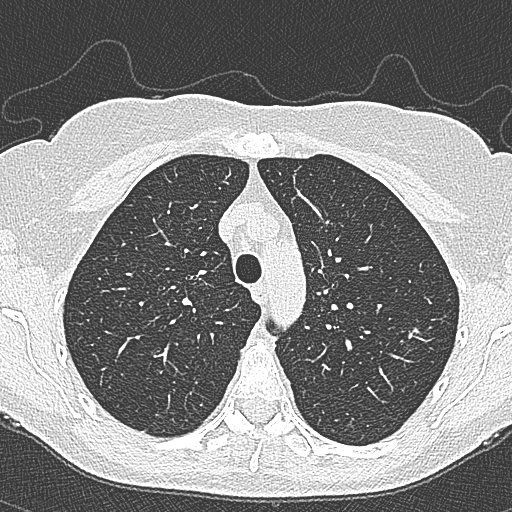
Chest CT (low-dose screening protocol), one axial image. Second annual screen. Lung window (W 1500 / L -600 HU). 1 mm slice thickness. Lung (sharp) reconstruction kernel (B80f). 120 kVp. Slice 82 of 350 in the series. Female participant, aged 65 years at enrolment. Current smoker at enrolment.
• Lesion marked by an expert reader, box from (x=397, y=312) to (x=446, y=362) px.
• The screening reader recorded 4 non-calcified nodules or masses ≥4 mm on this exam (left upper lobe, left upper lobe, left upper lobe, right lower lobe); which of them this box marks is not recorded.
• Official screen result: positive, change unspecified: nodule(s) >= 4 mm or enlarging nodule(s), mass(es), or other non-specific abnormalities suspicious for lung cancer.
• Participant outcome: lung cancer diagnosed 54 days after this screen — bronchiolo-alveolar carcinoma, non-mucinous, left upper lobe, stage IA (AJCC 6th edition), 10 mm at pathology.